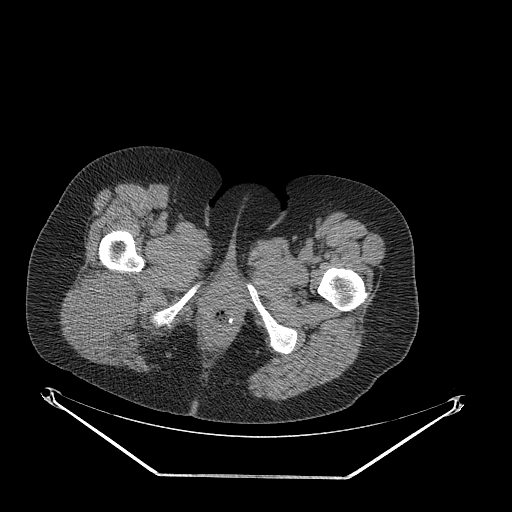
CT of an extremity soft-tissue mass (from a PET/CT study), one axial slice. Position 55 of 257 along the scan axis. Reconstruction kernel STANDARD. 140 kVp. Soft-tissue window (W 400 / L 40 HU). 512 × 512 image matrix. Female patient. From the clinical record (not read from this slice): histological type: synovial sarcoma; grade: intermediate; site of the primary tumour: right buttock.
Outlined on this slice (expert contour drawn on MRI and transferred to this co-registered scan by the dataset authors):
- gross tumour volume including surrounding oedema: bounding box (x1, y1, x2, y2) in pixels: (75, 267, 142, 353)
- gross tumour volume (mass): (75, 267, 142, 344)